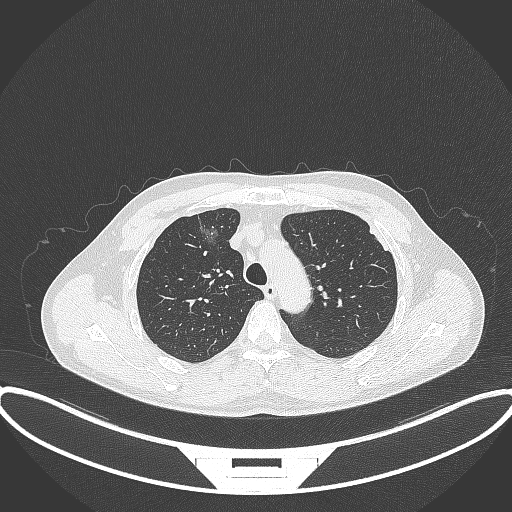
Chest CT, one axial slice. Position 275 of 395 along the scan axis. Reconstruction kernel B70f. 120 kVp. Lung window (W 1500 / L -600 HU). 1 mm slice thickness. 512 × 512 image matrix, field of view 424 × 424 mm. Patient: male, 60 years. Case-level facts recorded for this patient, not image findings: clinical TNM (as recorded): T1c N0 M0.
Outlined on this slice (rectangle marked by the reading radiologist):
- lung tumour (recorded histology: adenocarcinoma): bounding box (x1, y1, x2, y2) in pixels: (196, 215, 223, 253)